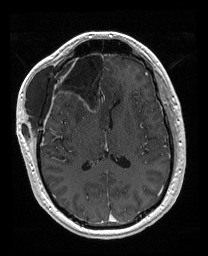
Brain MRI from a brain-tumour surgery series, one axial slice. Slice 87 of 176 in the series (ordered by position). T1-weighted post-contrast. 1 mm slice thickness. 208 × 256 image matrix, field of view 208 × 256 mm. From the clinical record (not read from this slice): histopathology: Astrocytoma; WHO grade: 4; IDH mutation: yes; tumour location: Right Orbitofrontal Anterior Temporal Insular.
Outlined on this slice (expert manual segmentation):
- previous resection cavity: bounding box [x1, y1, x2, y2] px = [56, 52, 106, 111]